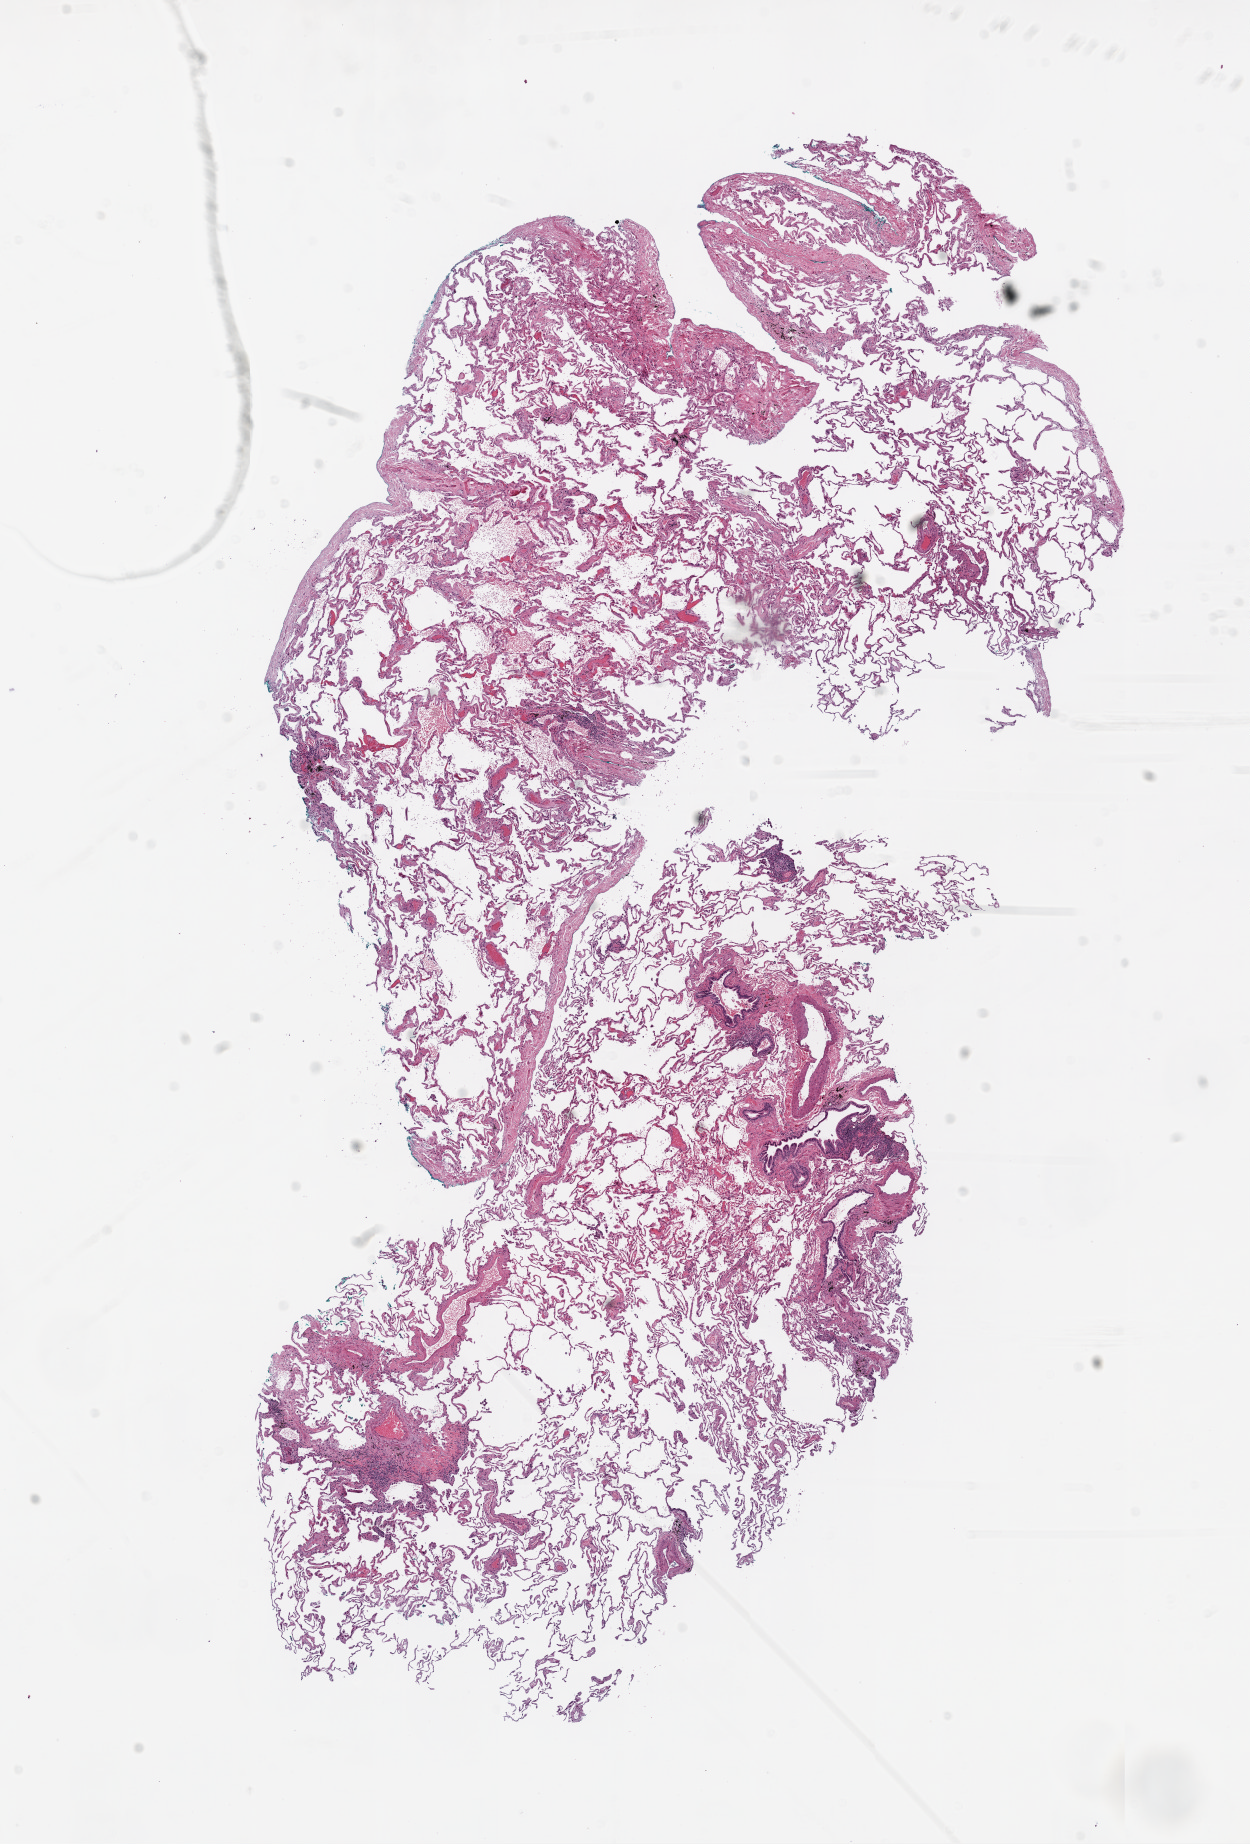
Whole-slide histology image, H&E-stained, a low-resolution overview of the entire scanned area, about 10.0 x 14.8 mm (acquisition: 20x scan), frozen section from the top of the tissue portion, solid tissue normal (non-tumour tissue) sample from the lung. Female patient; age at initial diagnosis 71 years.
This section: solid tissue normal sample (biorepository sample class). Patient diagnosis: Adenocarcinoma, NOS (upper lobe, lung).